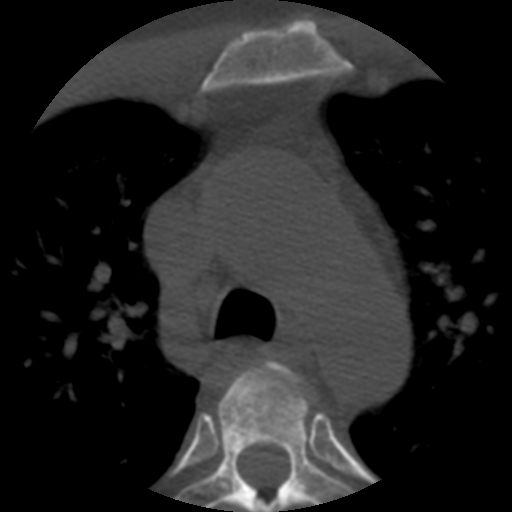
CT including the spine, one axial slice. Slice 399 of 508 in the series (ordered by position). Bone window (W 1800 / L 400 HU). 1.25 mm slice thickness. 512 × 512 image matrix, field of view 160 × 160 mm. Patient age 57 years. From the clinical record (not read from this slice): primary cancer: prostate.
Outlined on this slice (semi-automatic segmentation, software-assisted and operator-edited):
- T3 vertebra: box from (x=219, y=361) to (x=305, y=512) px
- T4 vertebra: (x=178, y=379)–(x=353, y=512)